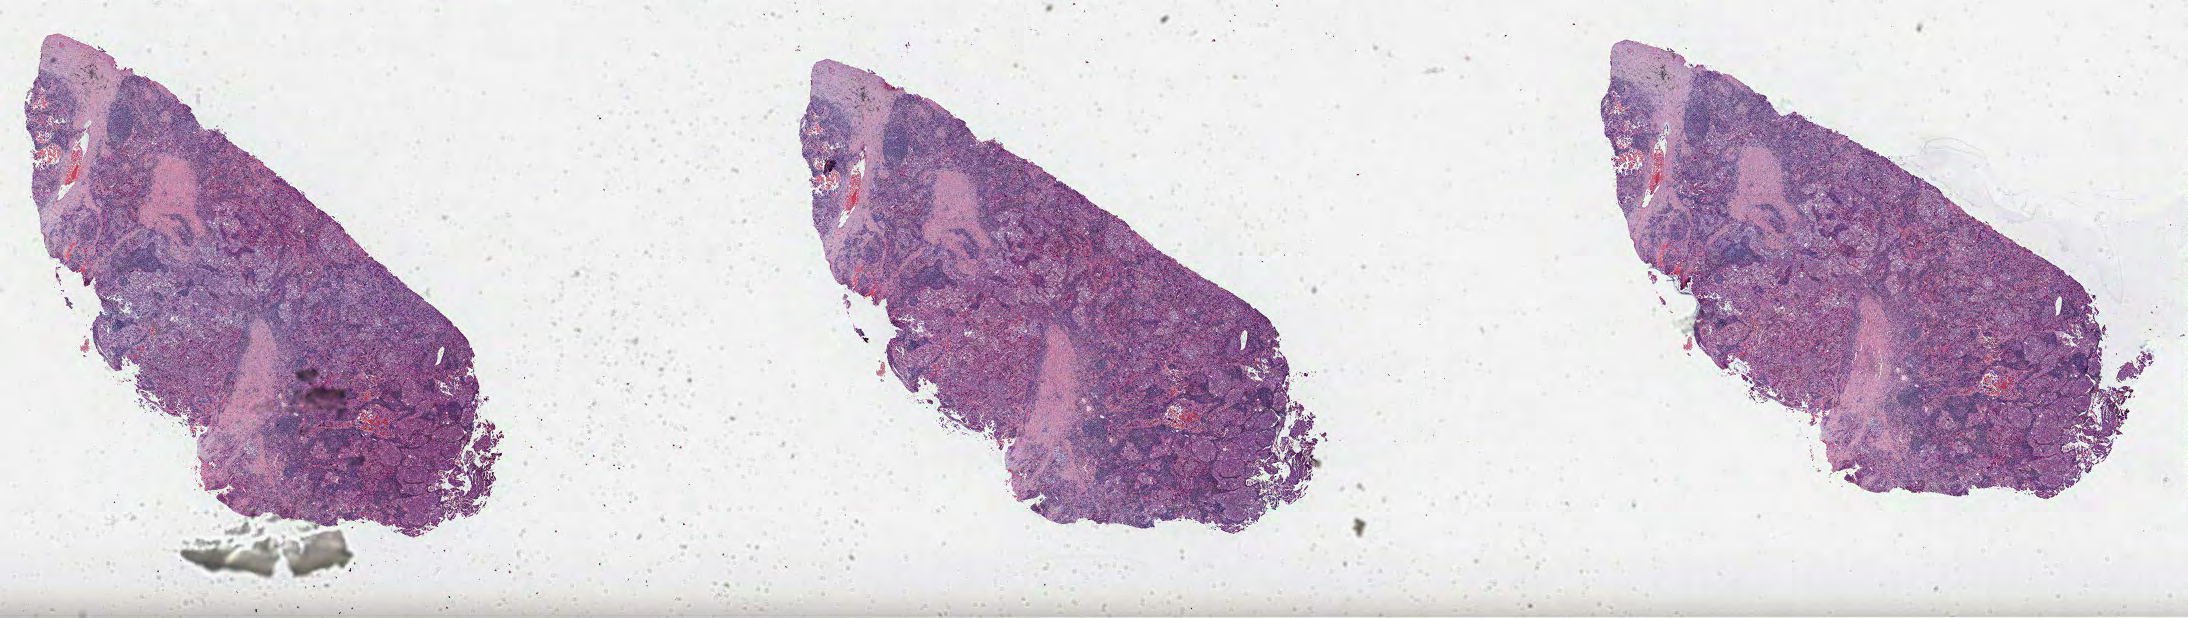
Whole-slide histology image, Hematoxylin and eosin (H&E) stained, low-resolution overview of the scanned area, about 35.3 x 10.0 mm (slide scanned at 40x), FFPE section, lung, primary tumour sample. Patient: male, age at initial diagnosis 78 years.
- AJCC pathologic stage: IIA (7th edition)
- laterality: right
- pathologic diagnosis: Squamous cell carcinoma, NOS (upper lobe, lung)
- TNM: T1b N1 M0